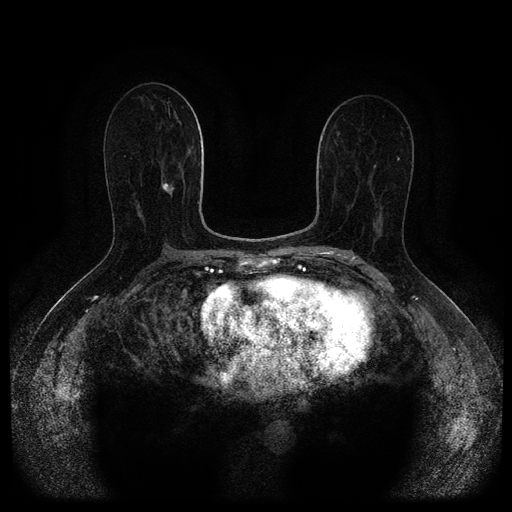
Breast MRI (dynamic contrast-enhanced, multi-phase), one axial slice. Slice 55 of 116 in the series (ordered by position). Dynamic contrast-enhanced series, time point 2 of 5 at this slice position (early post-contrast). 1.5 T. TE 2.7 ms, TR 5.4 ms. 2 mm slice thickness. 512 × 512 image matrix. Patient: female, 71 years.
Annotated regions visible in this slice (semi-automatic segmentation, software-assisted and operator-edited):
- breast lesion (labelled 'tumour' in the annotation; benign lesions carry a separate 'benign' label): bounding box [x1, y1, x2, y2] px = [162, 183, 175, 195]